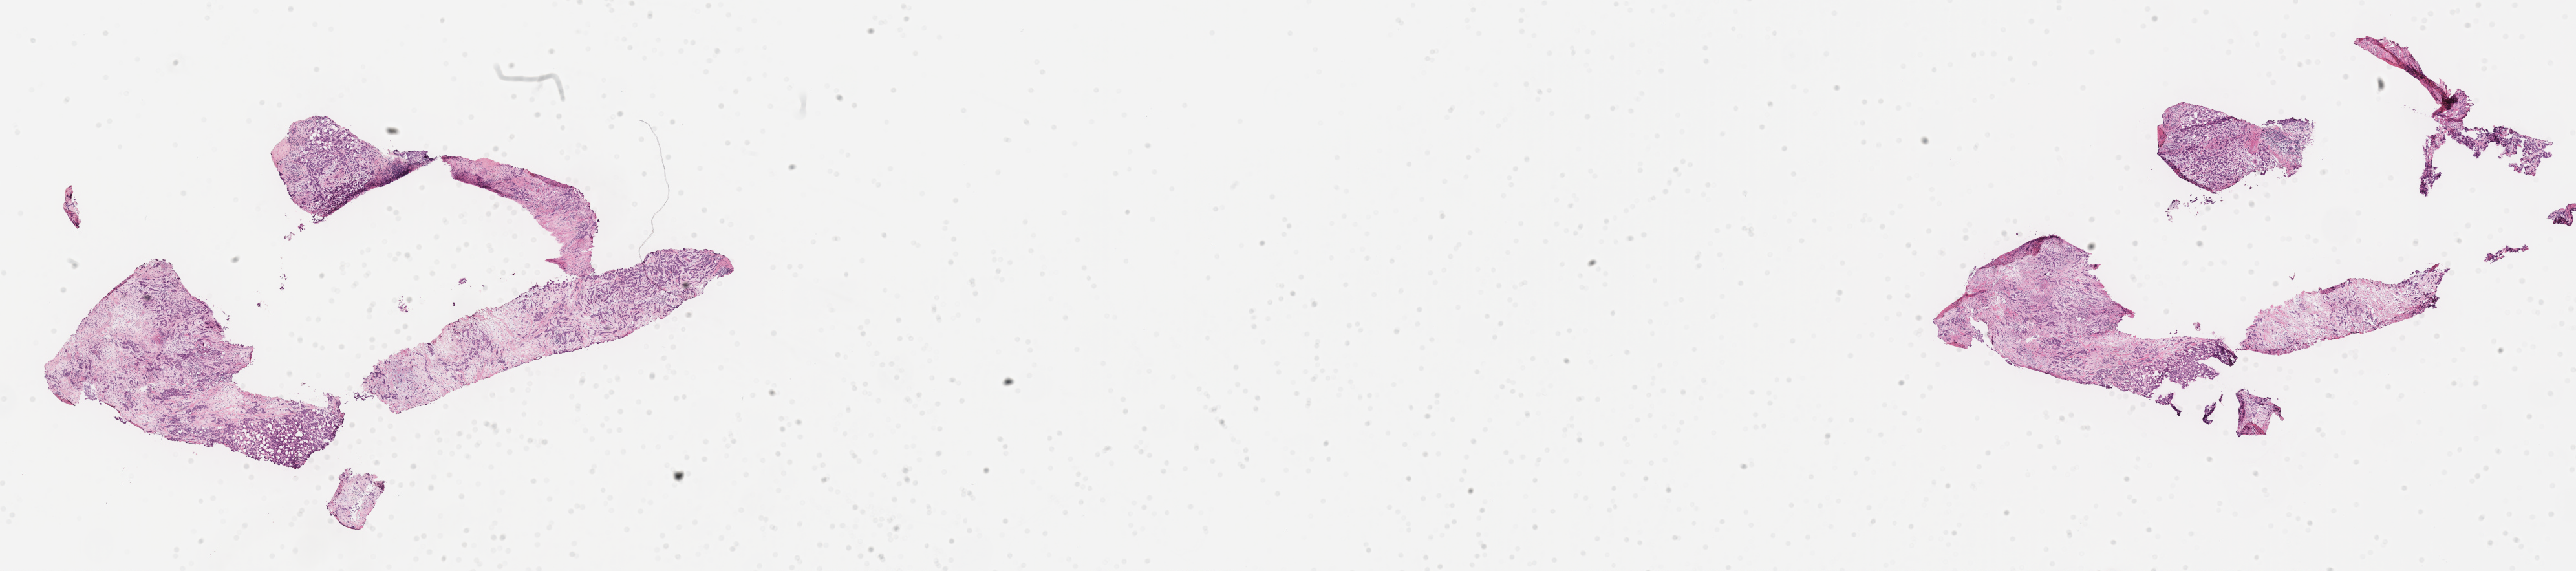
Digitized haematoxylin and eosin-stained section, shown as a low-resolution overview of the whole scanned area (about 32.1 x 7.1 mm), frozen section, primary tumor, site: breast. Patient: female, age at initial diagnosis 55 years. Composition of this section per pathologist review: tumor cells 30%, tumor nuclei 30%, stromal cells 60%, necrosis 0%, normal cells 10%. Infiltration values recorded for this section: lymphocyte infiltration 8%, monocyte infiltration 0%, neutrophil infiltration 2%.
* histologic diagnosis: Infiltrating duct carcinoma, NOS
* section: top of the tissue portion